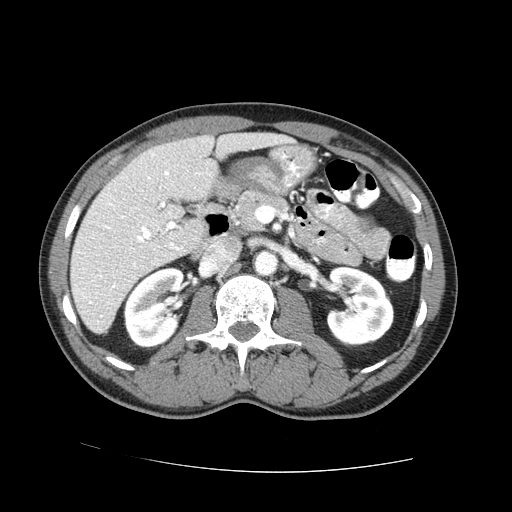
Contrast-enhanced abdominal CT (liver protocol), one axial slice; position 31 of 73 along the scan axis; reconstruction kernel STANDARD; 100 kVp; one of 2 acquisitions stored at this slice position; soft-tissue window (W 400 / L 40 HU); 2.5 mm slice thickness; 512 × 512 image matrix, field of view 380 × 380 mm. Case-level facts recorded for this patient, not image findings: diagnosis: hepatocellular carcinoma (patient treated with transarterial chemoembolisation; whether this scan precedes or follows treatment is not stated here); TNM stage (as recorded): Stage-IVA; Child-Pugh class: A; tumour nodularity: uninodular.
Structures marked on this image (semi-automatically segmented with operator editing):
- liver parenchyma outside the tumour (the mass and vessels are separate outlines, so this box may not span the whole liver): bounding box [x1, y1, x2, y2] px = [70, 132, 290, 332]
- liver vessels: [82, 154, 199, 304]